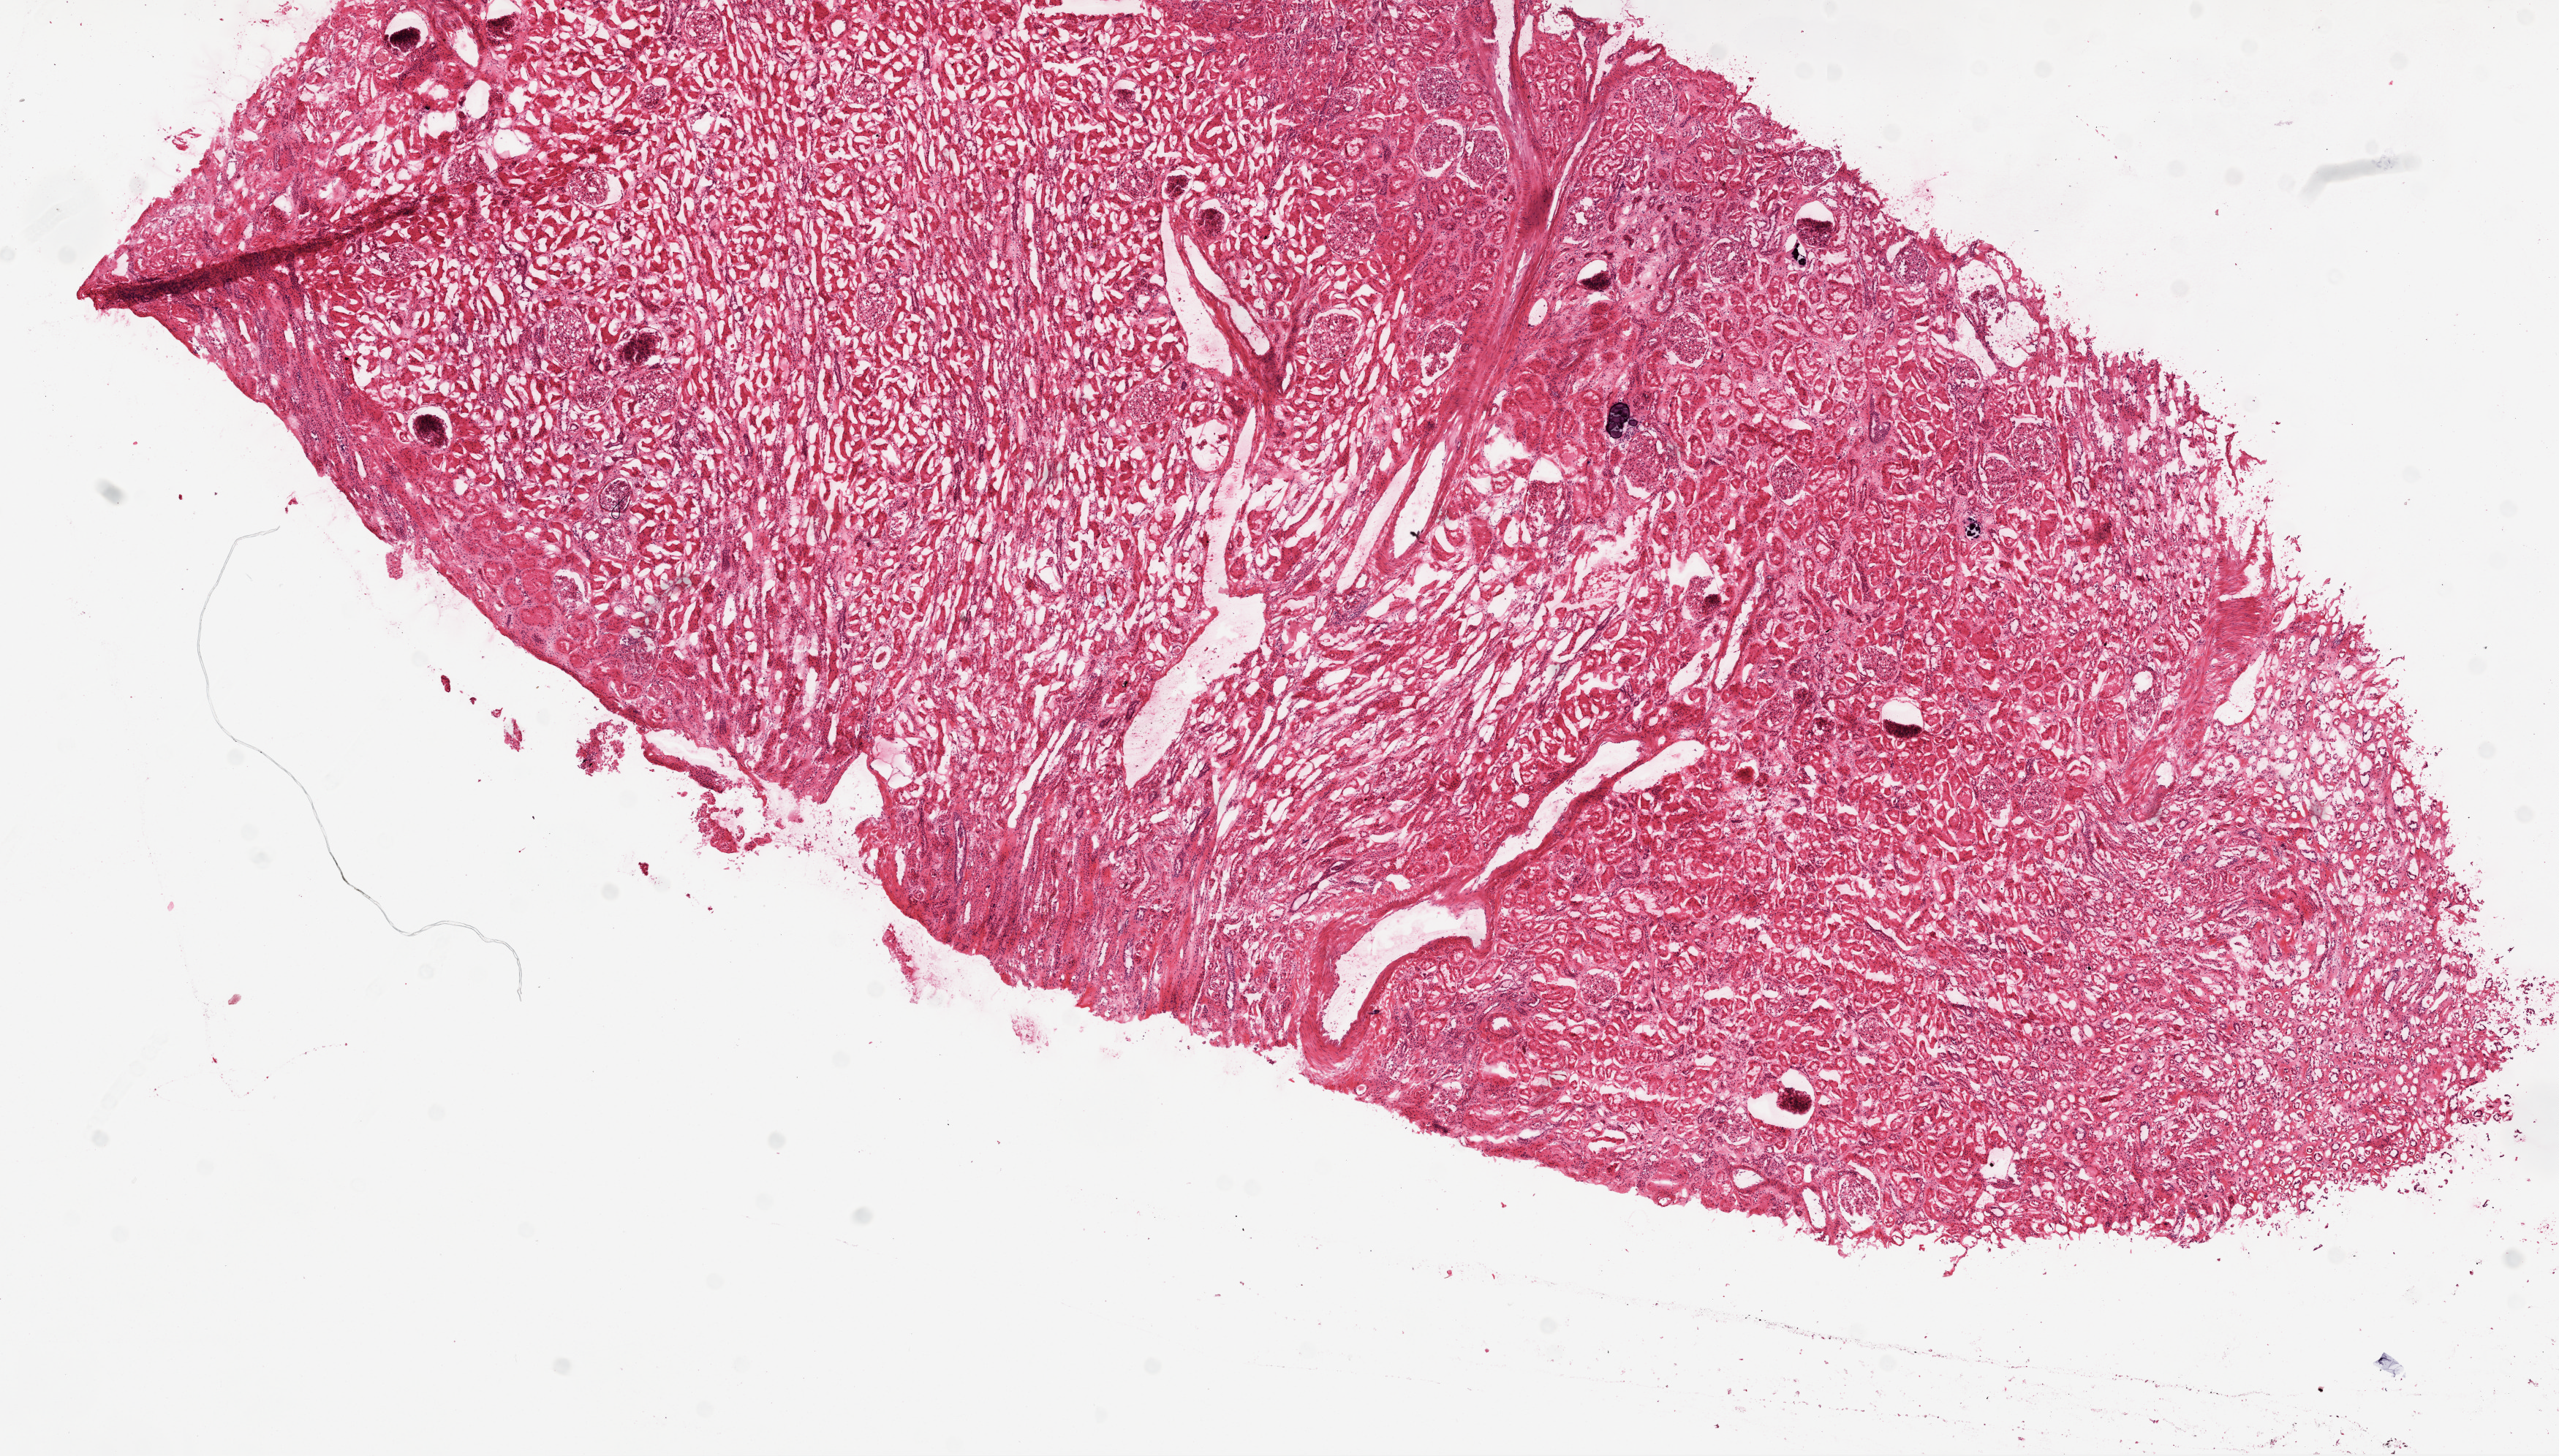
Digitized H&E-stained tissue section (whole slide), a low-resolution overview of the entire scanned area, about 14.0 x 8.0 mm (from a 20x scan), frozen section from the top of the tissue portion, sample: solid tissue normal (non-tumour tissue), kidney. Male, age 53 years at initial diagnosis.
This section: solid tissue normal (non-tumour) sample from the same patient. Patient diagnosis: Clear cell adenocarcinoma, NOS.